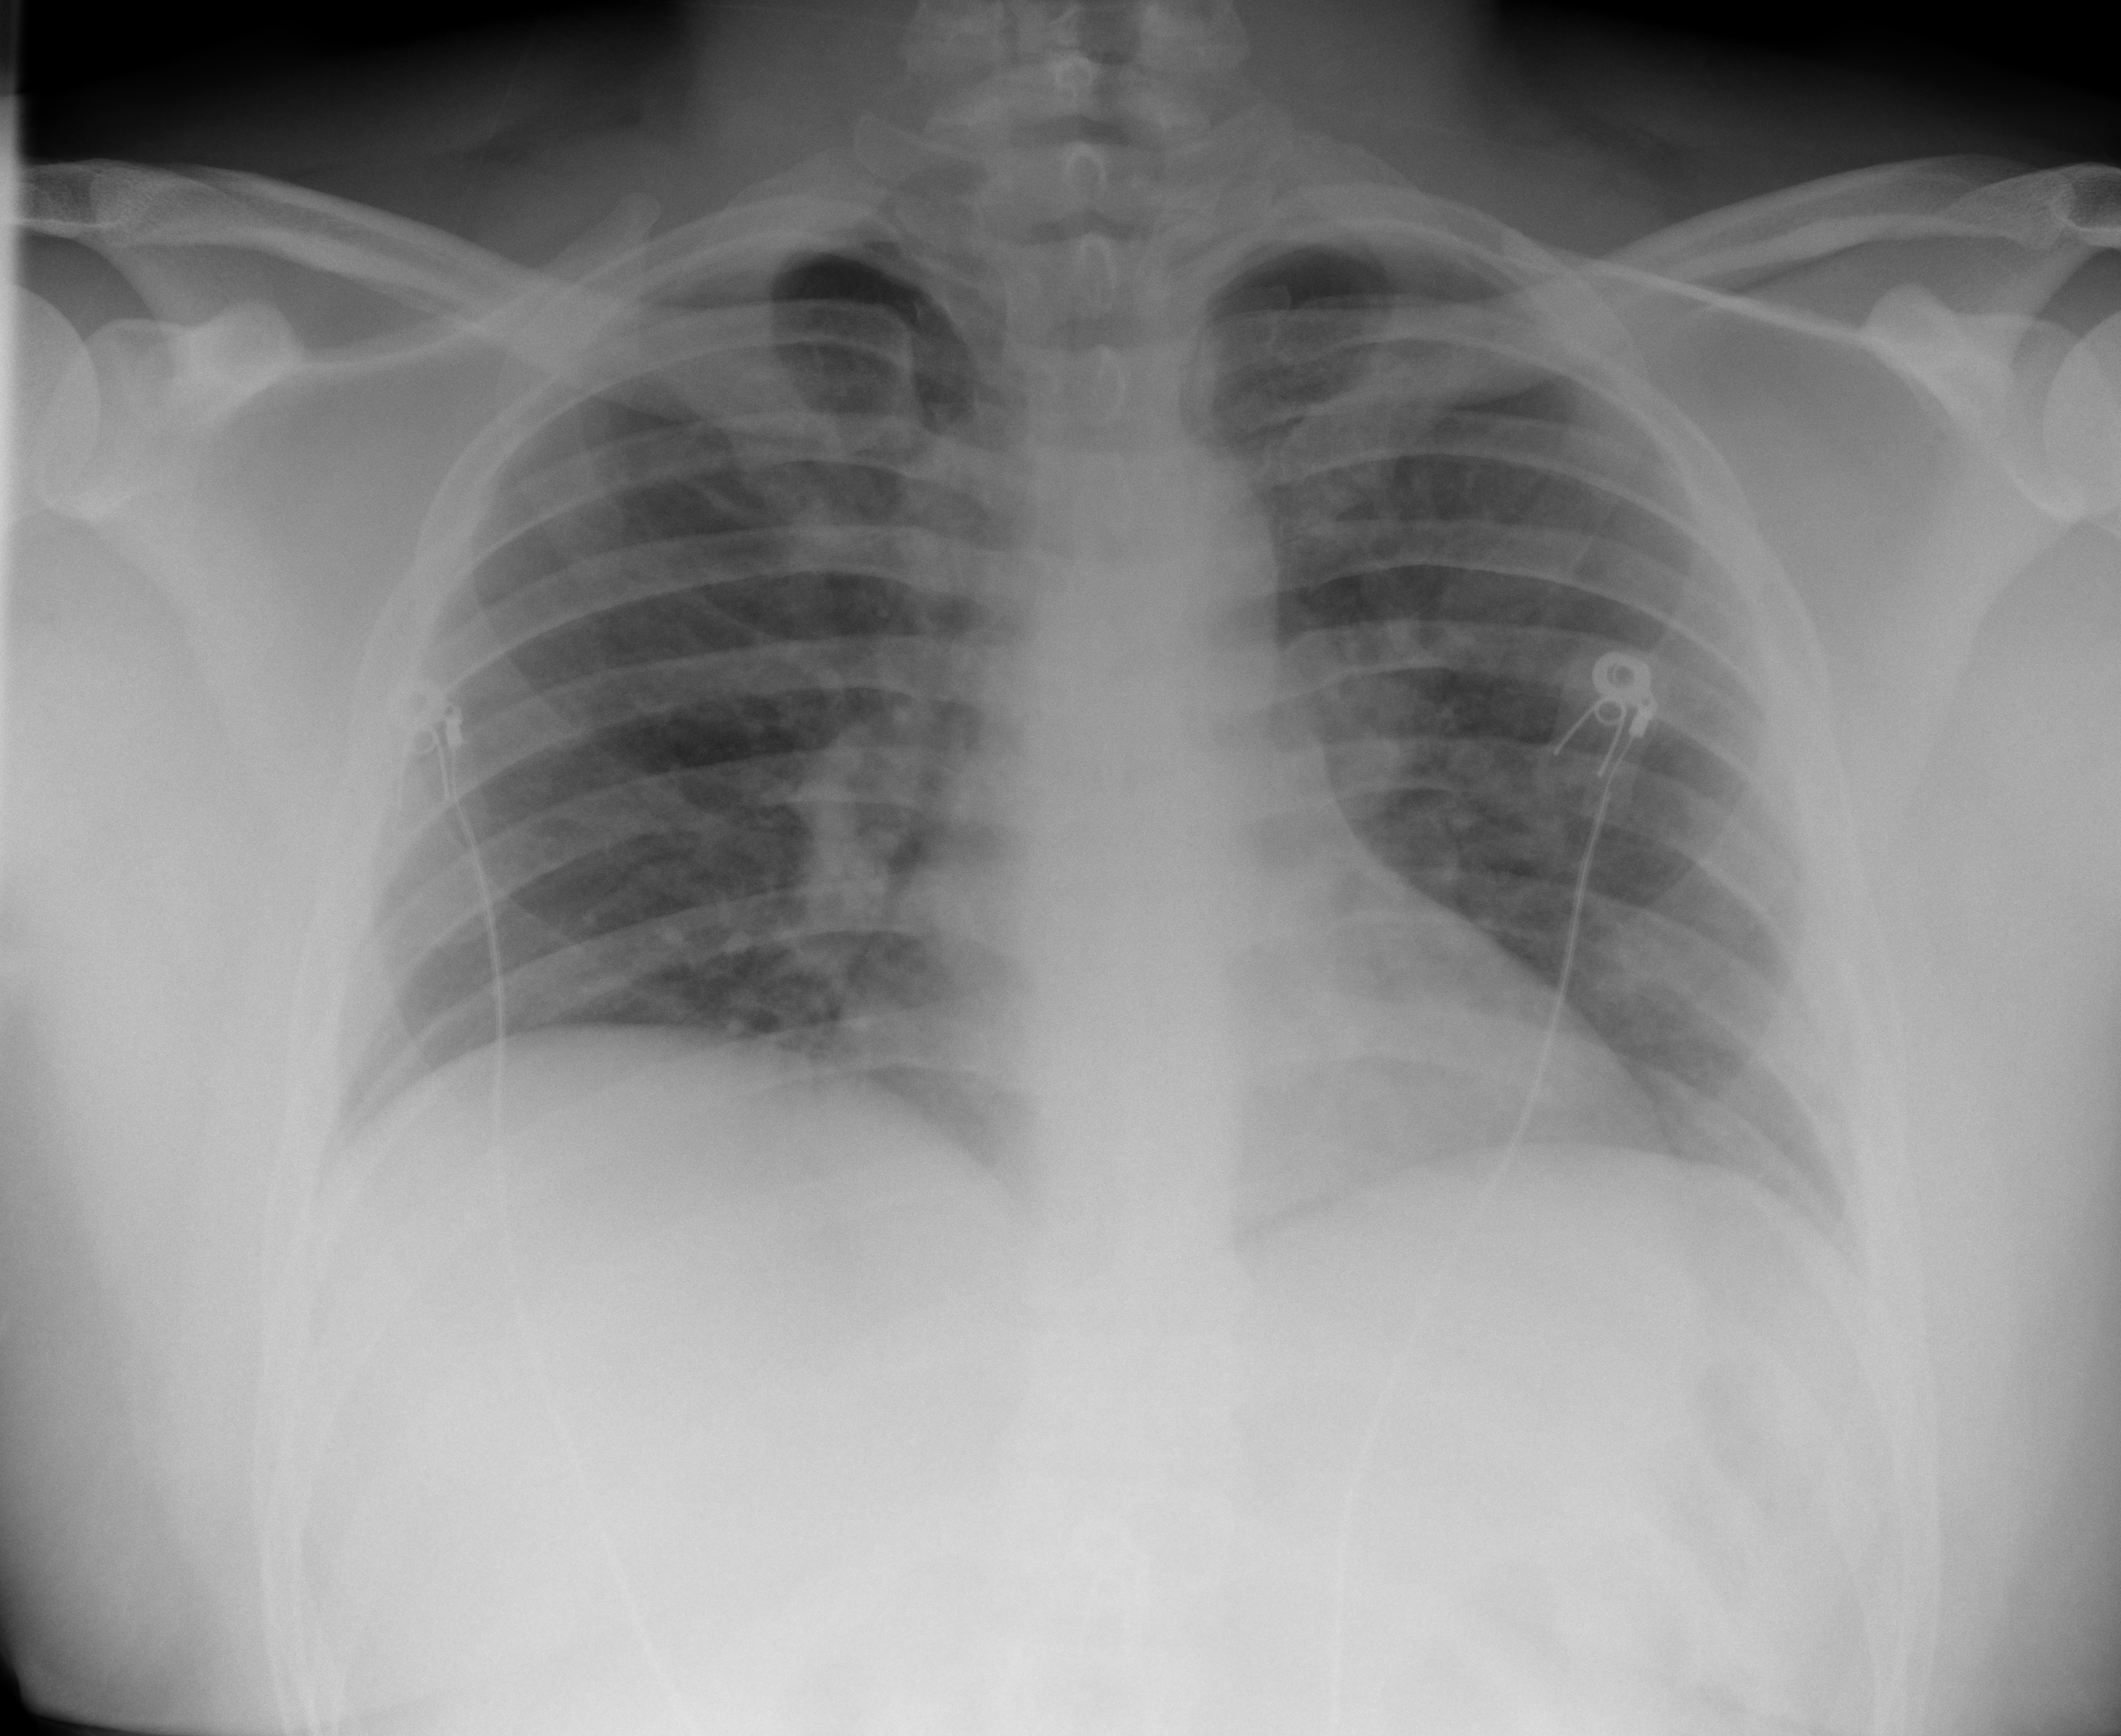
Chest X-ray (portable), AP projection. Male patient, age 31 years; imaged 7 days after the COVID-19 diagnosis.
Key findings recorded by the radiologist: atelectatic changes at the lung bases.